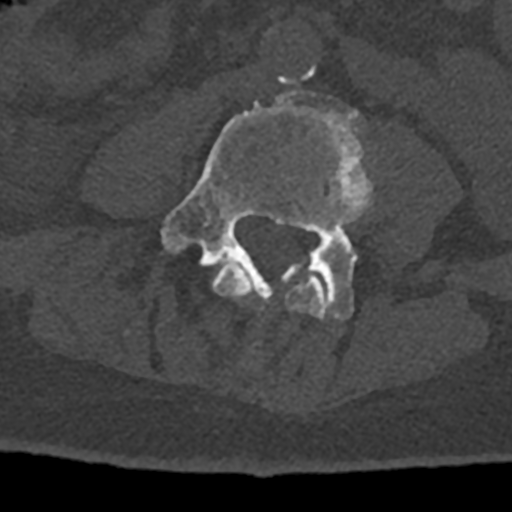
CT including the spine, one axial slice; slice 272 of 797 in the series (ordered by position); reconstruction kernel Br40s/3; bone window (W 1800 / L 400 HU); 0.5 mm slice thickness; 512 × 512 image matrix. Male patient, age 74 years. From the clinical record (not read from this slice): primary cancer: renal; vertebrae with lytic lesions (as recorded): T10, L1, L2, L3, L4, L5.
Annotated regions visible in this slice (semi-automatic segmentation, software-assisted and operator-edited):
- L3 vertebra: box from (x=212, y=262) to (x=327, y=319) px
- L4 vertebra: (x=160, y=85)–(x=372, y=321)